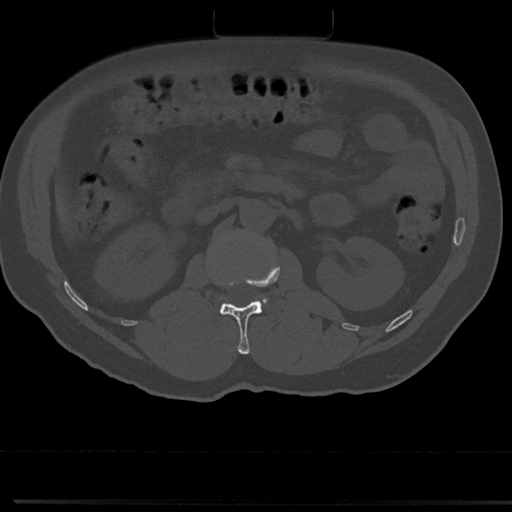
CT including the spine, one axial slice. Position 57 of 817 along the scan axis. 120 kVp. Bone window (W 1800 / L 400 HU). 0.5 mm slice thickness. 512 × 512 image matrix, field of view 355 × 355 mm. Patient: male, 61 years. Case-level facts recorded for this patient, not image findings: primary cancer: prostate.
Outlined on this slice (semi-automatic segmentation, software-assisted and operator-edited):
- L1 vertebra: box from (x=219, y=261) to (x=280, y=354) px